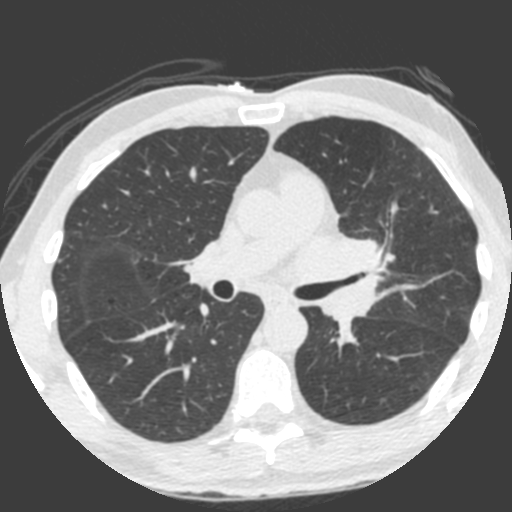
Chest CT (low-dose screening protocol), one axial image. Third annual screen. Lung window (W 1500 / L -600 HU). 2 mm slice thickness. Standard (soft-tissue) reconstruction kernel (B). 120 kVp. 512 × 512 image matrix, field of view 315 × 315 mm. Male participant, aged 55 years at enrolment. Current smoker at enrolment.
Lesion marked by an expert reader, bounding box [x1, y1, x2, y2] px = [309, 212, 401, 325]. Screening reader's record for this exam (one nodule recorded; not confirmed to be the boxed lesion): non-calcified nodule or mass ≥4 mm, left upper lobe, 49 × 29 mm, spiculated (stellate) margins, soft tissue attenuation, pre-existing on the prior screen: yes; interval growth: yes. Lung cancer was diagnosed 0 days after this screen: small cell carcinoma, NOS, left upper lobe, undifferentiated (G4), stage IV (AJCC 6th edition), 60 mm at pathology.